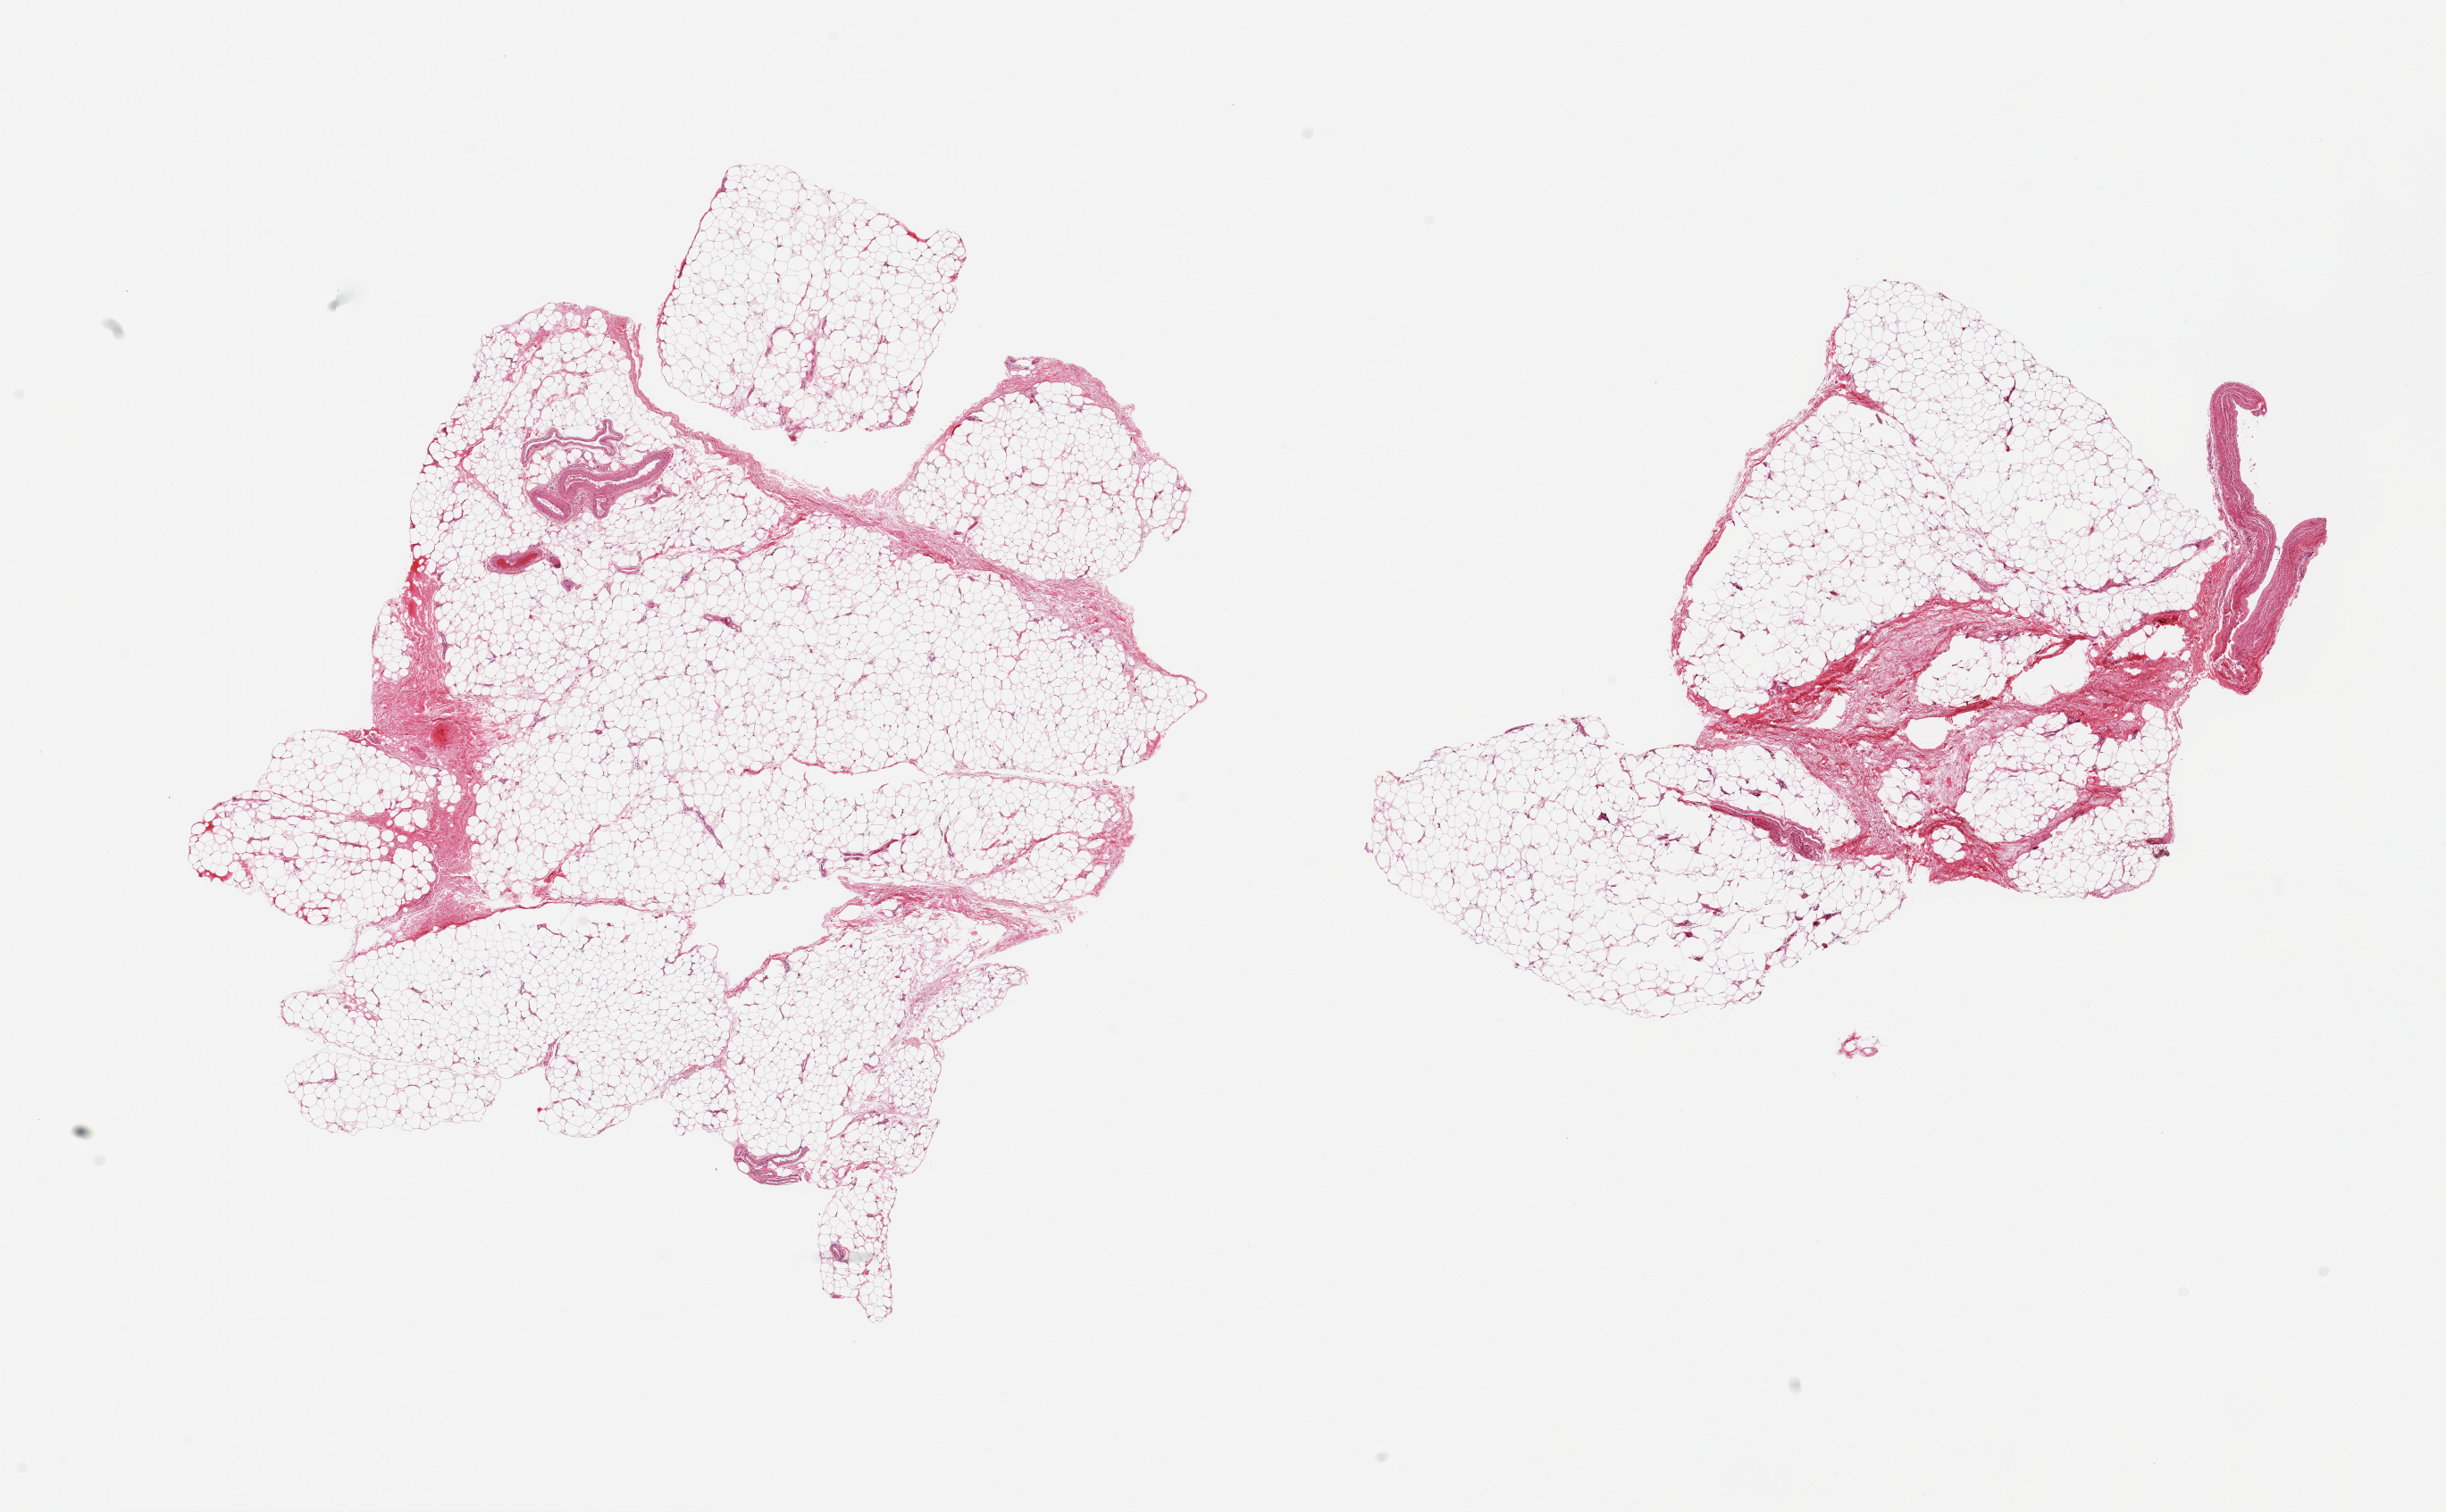
Digitized H&E-stained section, brightfield — whole scanned area (about 21.7 x 13.4 mm, slide scanned at 20x) shown as a low-resolution overview, PAXgene-fixed, paraffin-embedded tissue, sampled site (target tissue): adipose tissue, tissue donor sample. Donor sex: female.
• review note (as recorded): 2 pieces; 1 with 10% fibrous content